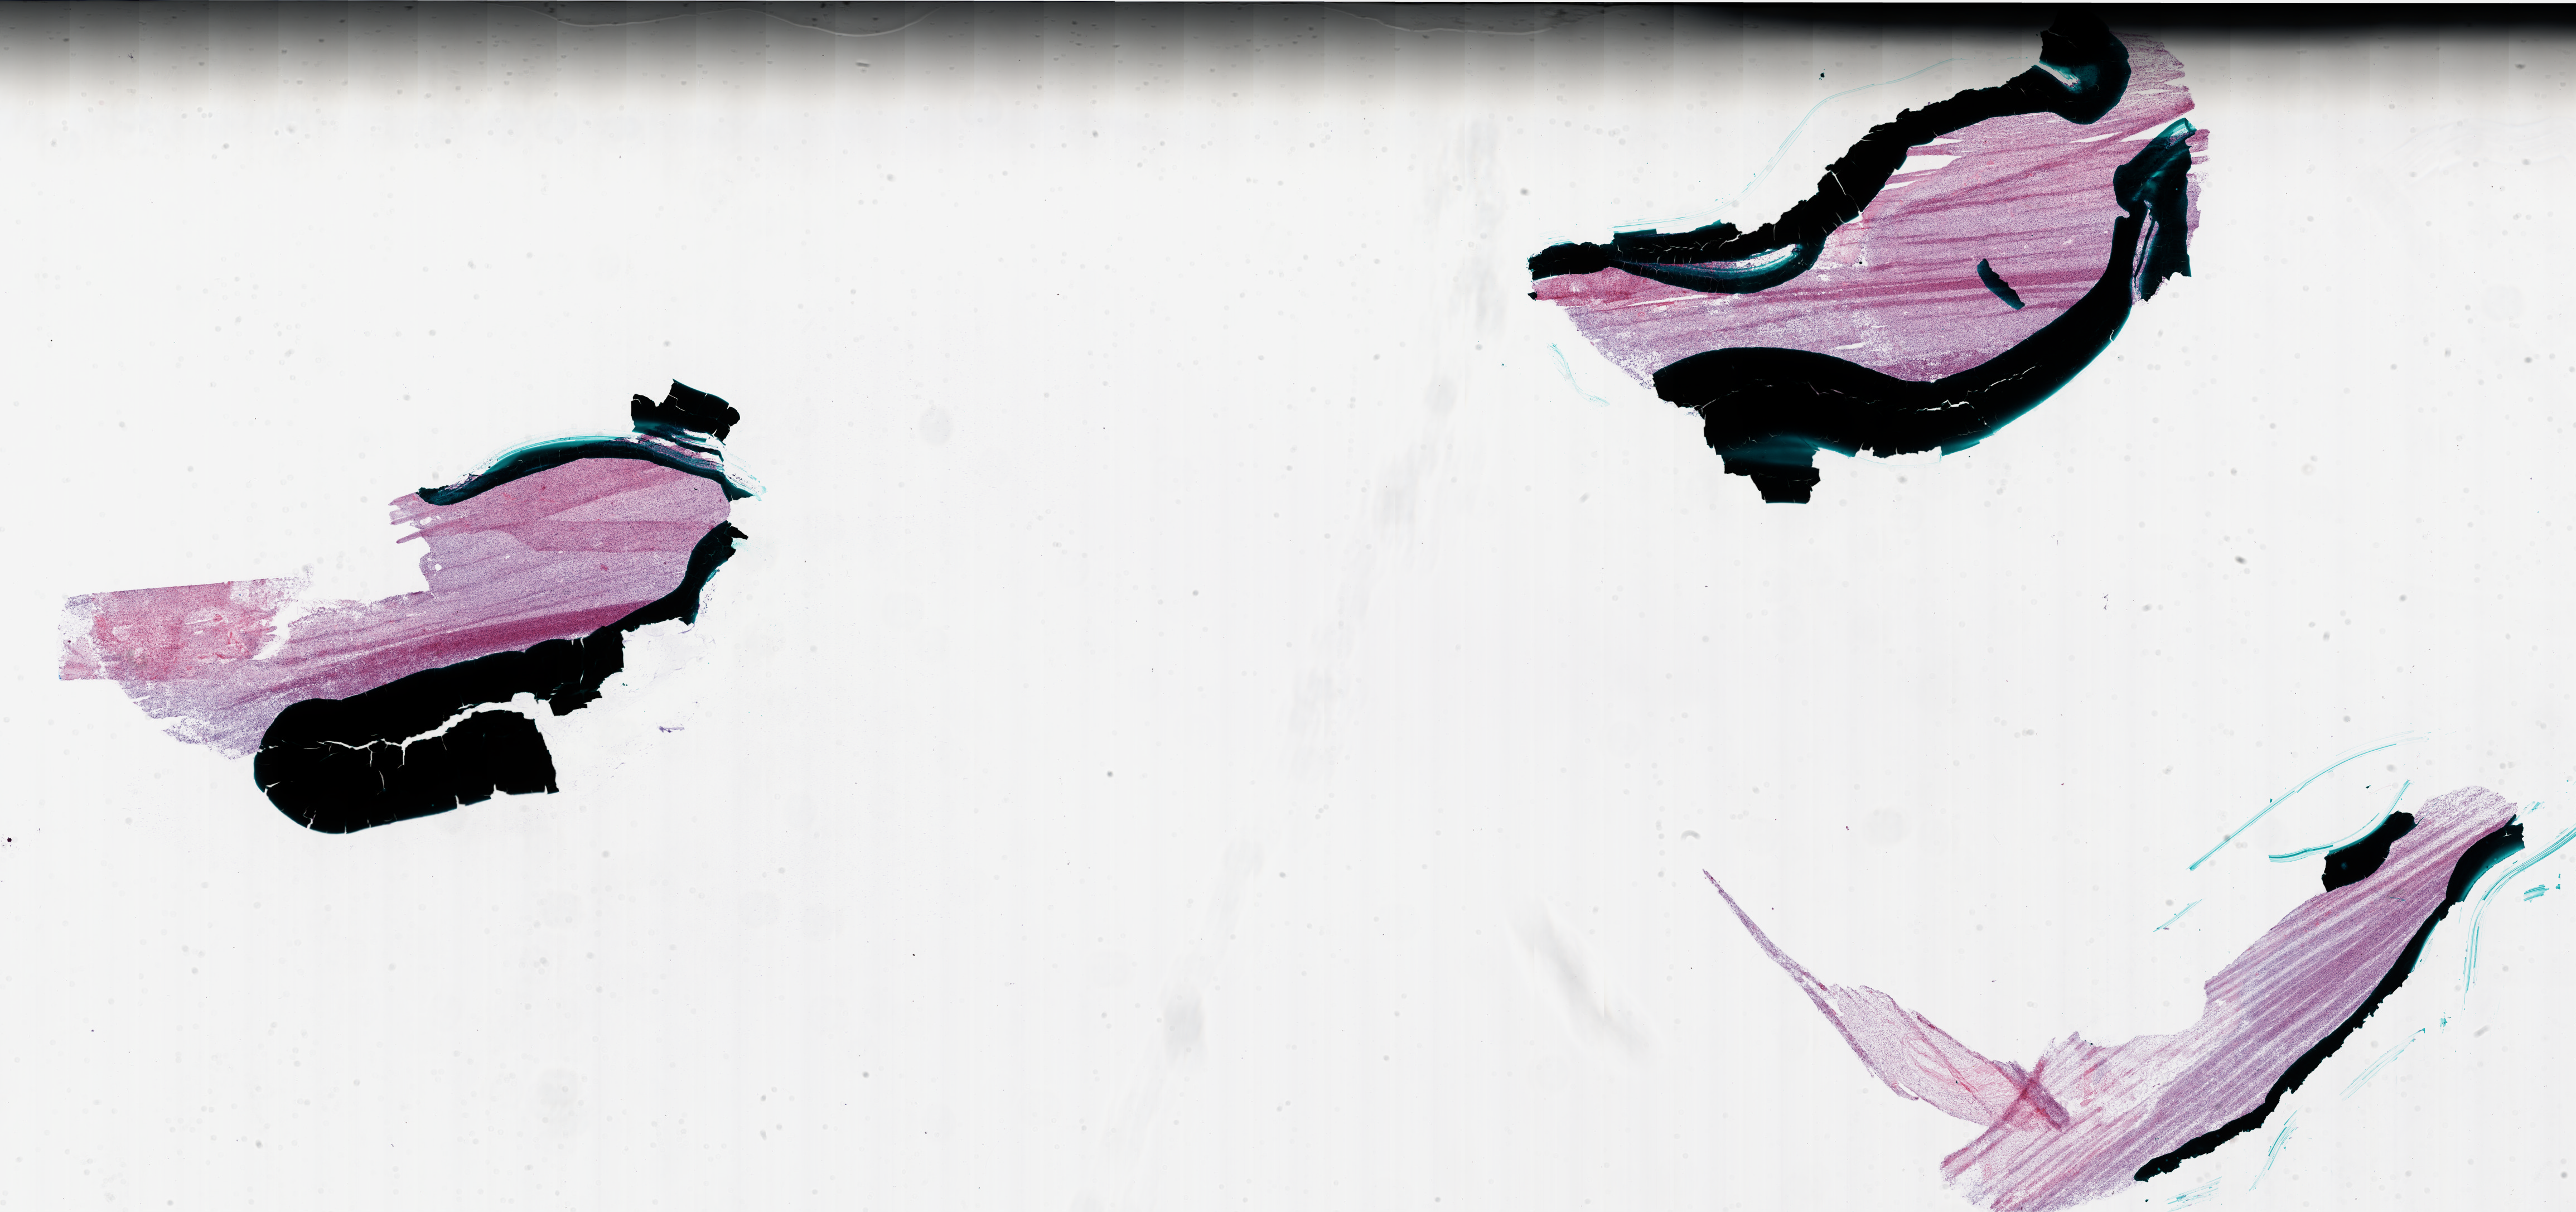
Whole-slide histology image, H&E-stained, whole scanned area (about 37.0 x 17.4 mm, from a 20x scan) shown as a low-resolution overview, frozen section, brain, primary tumour sample. Patient: male, age at initial diagnosis 57 years. Slide review estimates, as recorded: tumour cells 95%, tumour nuclei 100%, normal cells 0%, stromal cells 0%, necrosis 5%.
Diagnosis: Glioblastoma.